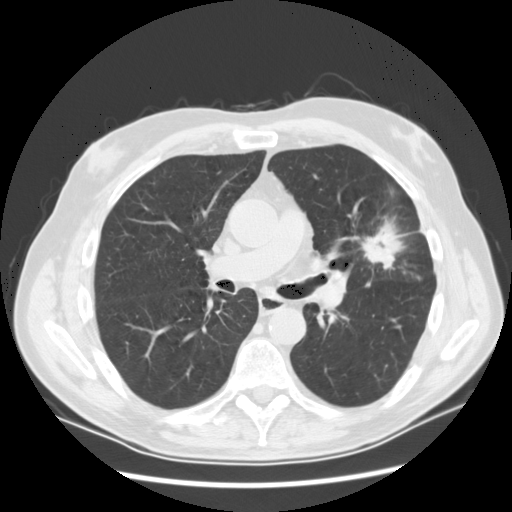
Low-dose screening chest CT, axial slice, first (baseline) screen, lung window (W 1500 / L -600 HU), standard (soft-tissue) reconstruction kernel (STANDARD), slice 57 of 132 in the series. Male participant, aged 65 years at enrolment. Current smoker at enrolment.
Expert-annotated lung lesion, bounding box <350,217,416,285> (left, top, right, bottom; pixels). The exam's reader record, not a measurement of the box and not confirmed to be the same lesion: non-calcified nodule or mass ≥4 mm, left upper lobe, 37 × 27 mm, spiculated (stellate) margins, soft tissue attenuation. Official screen result: positive, change unspecified: nodule(s) >= 4 mm or enlarging nodule(s), mass(es), or other non-specific abnormalities suspicious for lung cancer. Participant outcome: lung cancer diagnosed 56 days after this screen — non-small cell carcinoma, poorly differentiated (G3), stage IA (AJCC 6th edition).